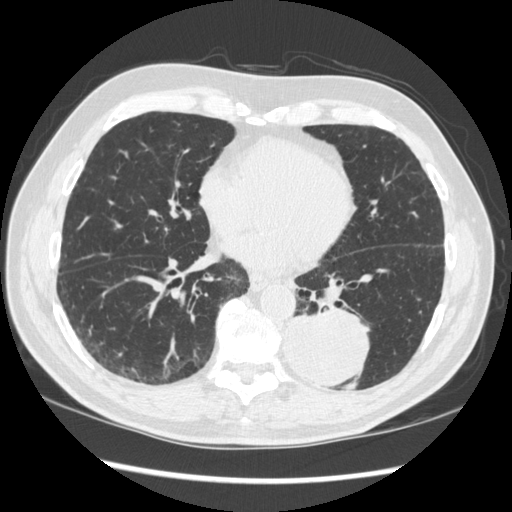
Low-dose screening chest CT, one axial slice. Position 132 of 348 along the scan axis. Reconstruction kernel STANDARD. 120 kVp. Lung window (W 1500 / L -600 HU). 1.25 mm slice thickness. 512 × 512 image matrix, field of view 360 × 360 mm.
Outlined on this slice (expert manual segmentation):
- lesion 1 (tumor, lower lobe of left lung): box from (x=284, y=310) to (x=369, y=389) px